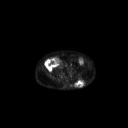
FDG PET of an extremity soft-tissue mass (from a PET/CT study), one axial slice. 3.27 mm slice thickness. 128 × 128 image matrix, field of view 700 × 700 mm. Patient: male, 69 years. From the clinical record (not read from this slice): histological type: leiomyosarcoma; grade: intermediate; site of the primary tumour: left pelvis.
Annotated regions visible in this slice (expert contour drawn on MRI and transferred to this co-registered scan by the dataset authors):
- gross tumour volume (mass): bounding box [x1, y1, x2, y2] px = [75, 78, 85, 88]